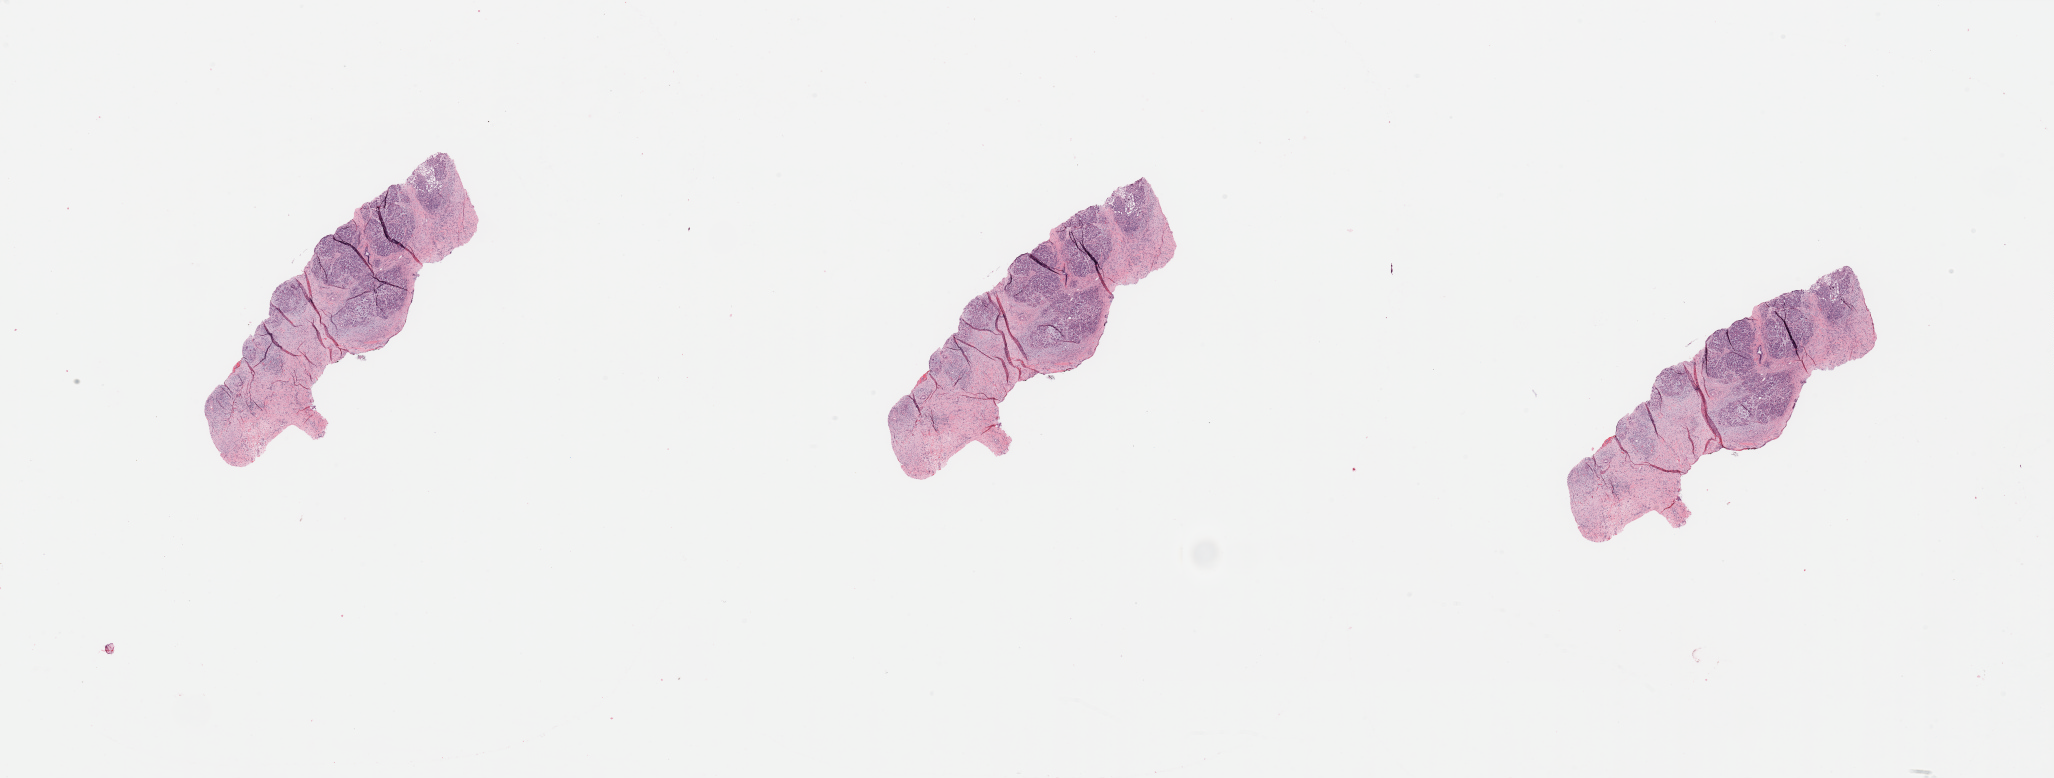
Digitized Hematoxylin and eosin (H&E) stained tissue section (whole slide) — whole scanned area (about 32.5 x 12.3 mm, slide scanned at 20x) shown as a low-resolution overview. Normal (non-tumour) tissue sample, sampled site: pancreas. 68-year-old female patient.
* this section: normal (non-tumour) tissue from the same patient
* patient diagnosis: Infiltrating duct carcinoma, NOS